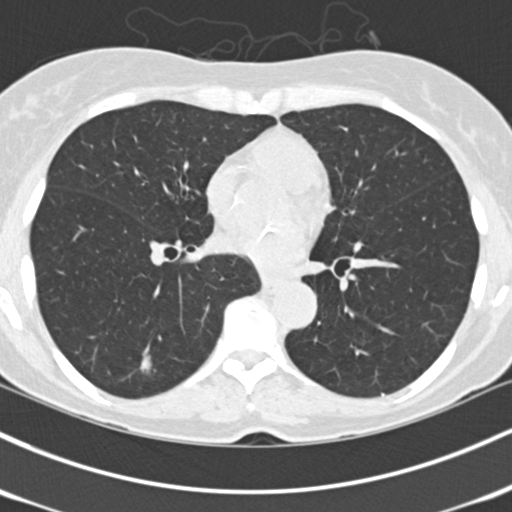
Low-dose screening chest CT, one axial slice; slice 66 of 150 in the series (ordered by position); lung window (W 1500 / L -600 HU); 2 mm slice thickness; 512 × 512 image matrix, field of view 318 × 318 mm.
Outlined on this slice (expert manual segmentation):
- lesion 1 (tumor): bounding box (x1, y1, x2, y2) in pixels: (140, 357, 151, 372)